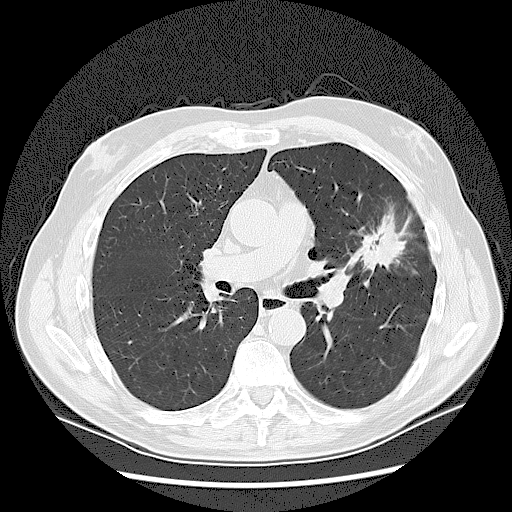
Low-dose screening chest CT, axial slice; first (baseline) screen; lung window (W 1500 / L -600 HU). Male participant, aged 65 years at enrolment. Current smoker at enrolment.
- Expert-annotated lung lesion, bounding box (x1, y1, x2, y2) in pixels: (349, 224, 398, 269).
- The exam's reader record, not a measurement of the box and not confirmed to be the same lesion: non-calcified nodule or mass ≥4 mm, left upper lobe, 37 × 27 mm, spiculated (stellate) margins, soft tissue attenuation.
- Participant outcome: lung cancer diagnosed 56 days after this screen — non-small cell carcinoma, poorly differentiated (G3), stage IA (AJCC 6th edition).